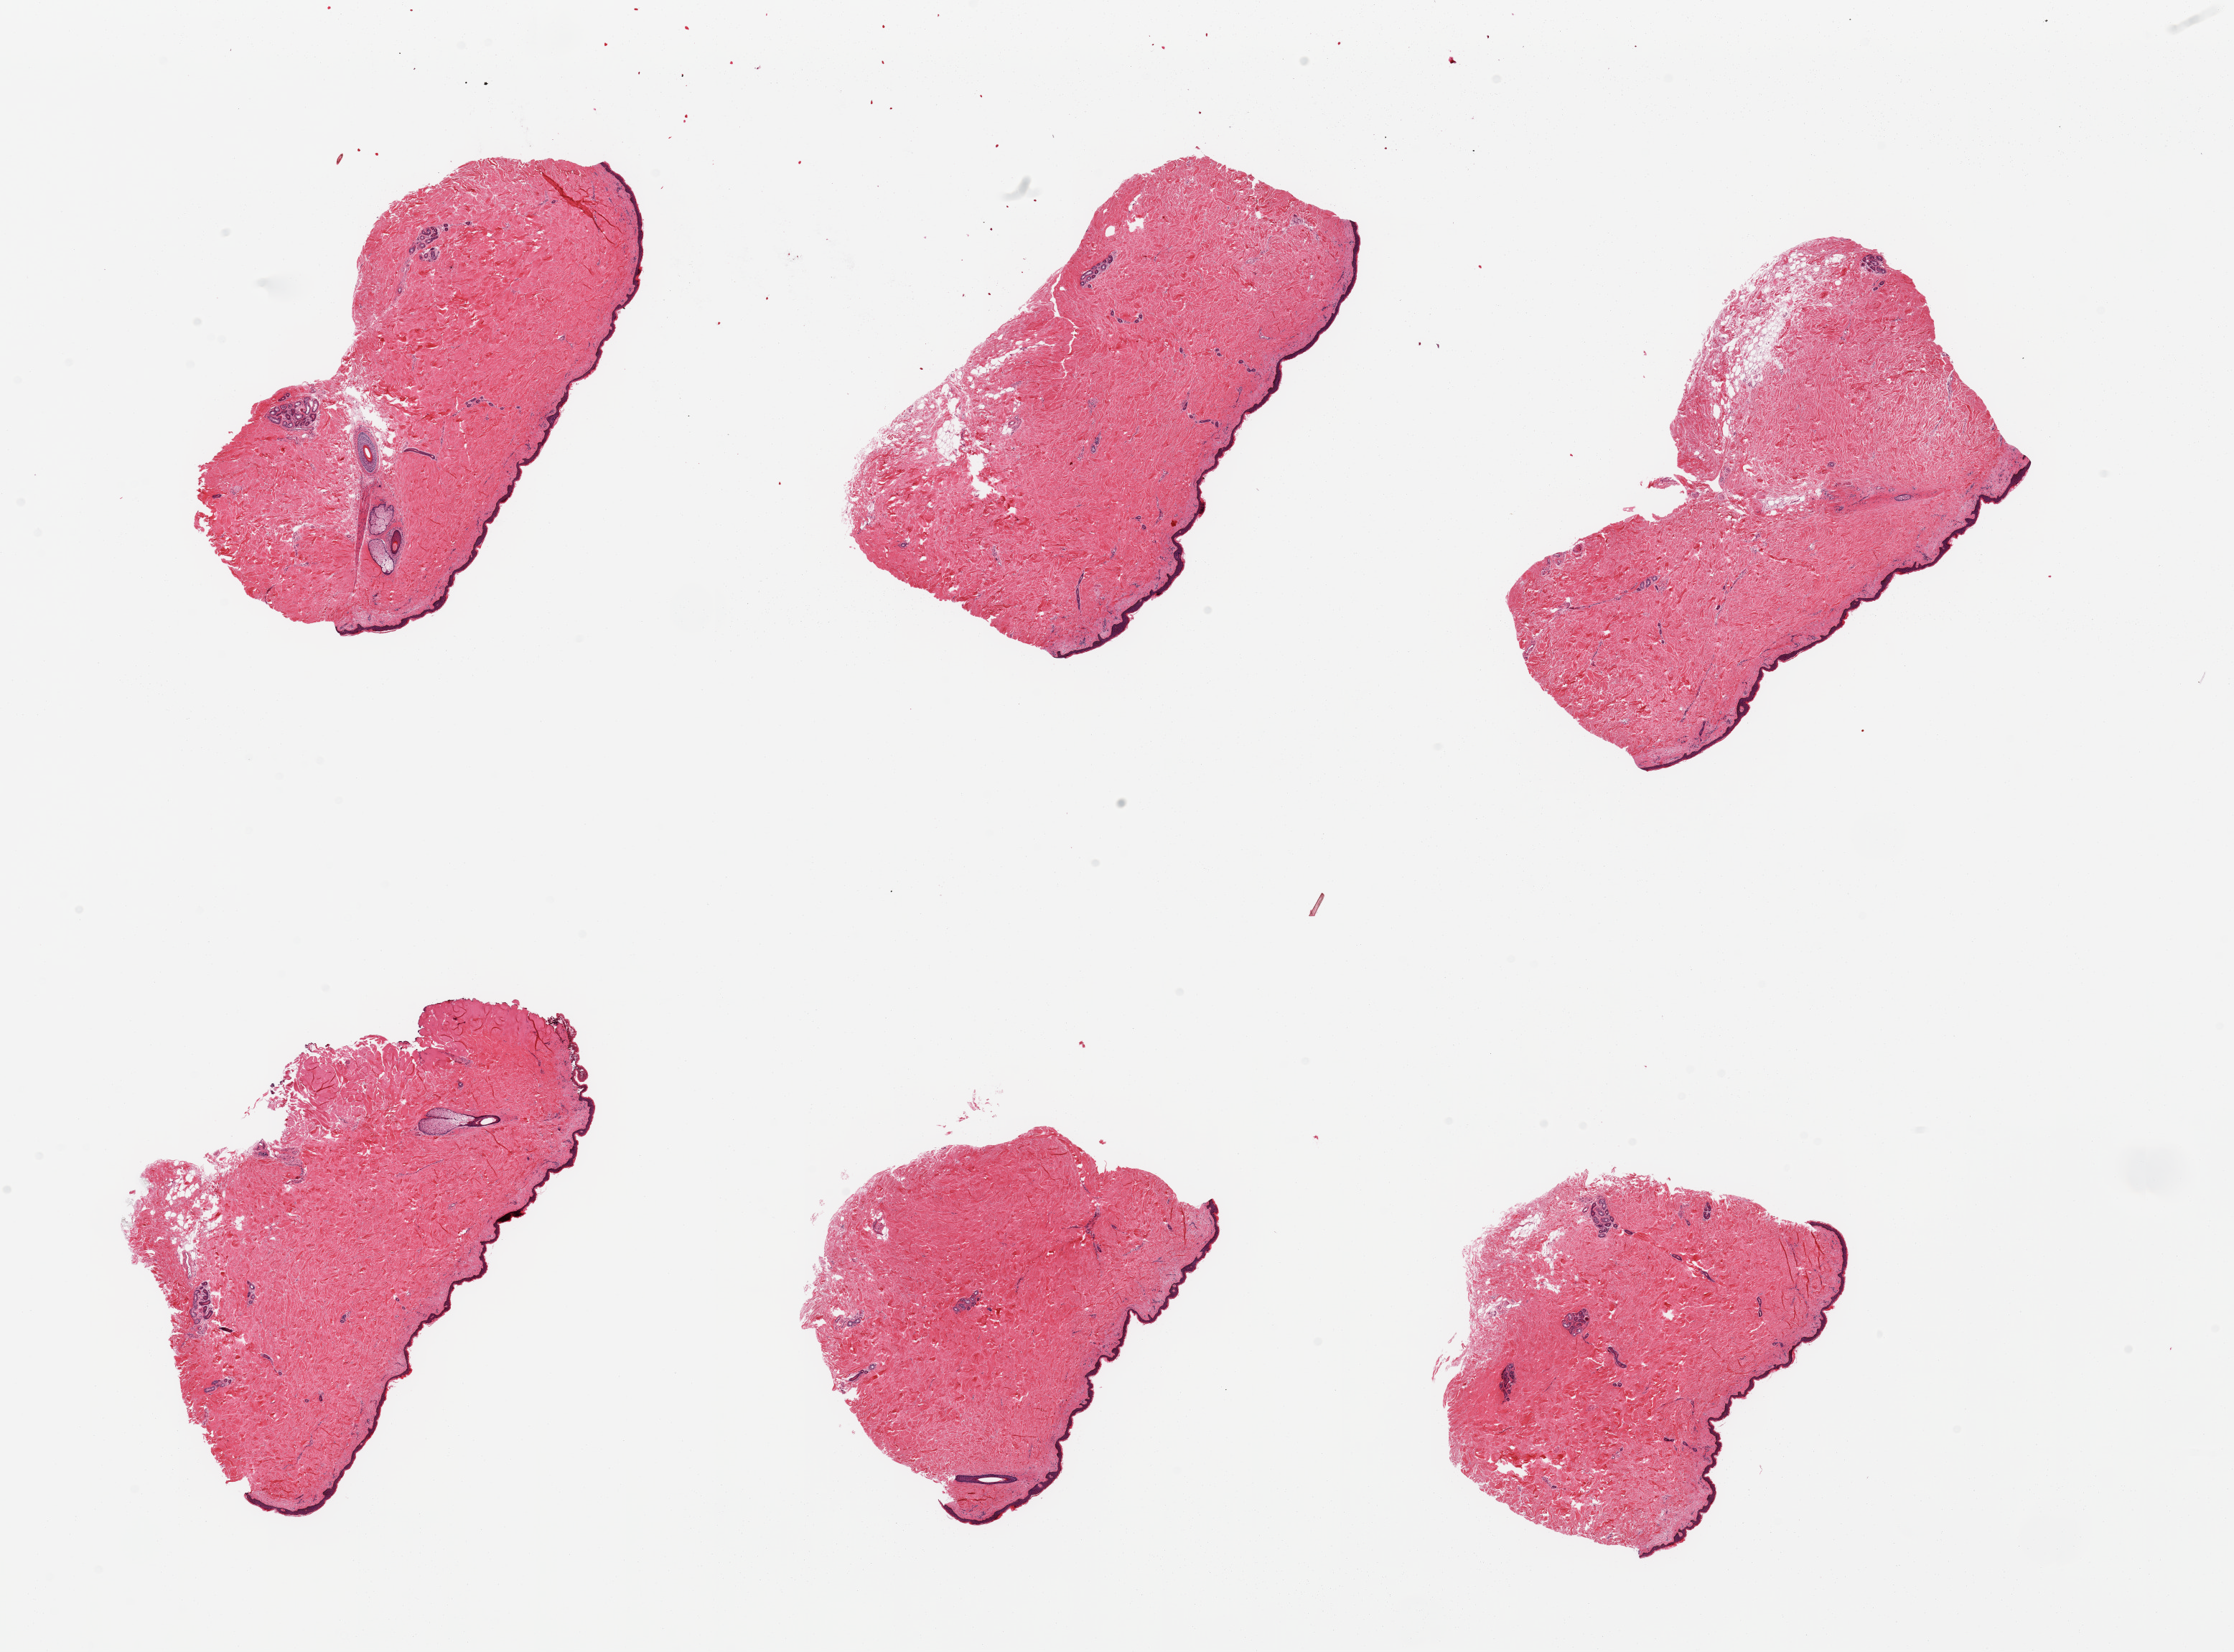
Hematoxylin and eosin (H&E) whole-slide image, shown as a low-resolution overview of the whole scanned area (about 24.6 x 18.2 mm). PAXgene-fixed, paraffin-embedded tissue. Sampled site (target tissue): skin of suprapubic region. Donor tissue sample. Donor sex: male.
- reviewer comment on this tissue sample: 6 pieces, no dermal fat; squamous epithelium is ~50-60 microns